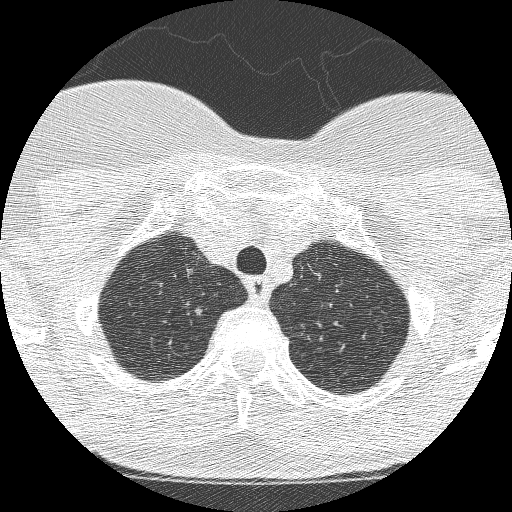
Low-dose screening chest CT, axial slice, second annual screen, lung window (W 1500 / L -600 HU), 1.25 mm slice thickness, lung (sharp) reconstruction kernel (BONE), 120 kVp, slice 210 of 250 in the series. Female, age 61 years at enrolment. Current smoker at enrolment.
- Expert-annotated lung lesion, bounding box (x1, y1, x2, y2) in pixels: (173, 295, 215, 330).
- Reader record for this screening exam (exam-level; its link to the box is not recorded): non-calcified nodule or mass ≥4 mm, right upper lobe, 11 × 8 mm, poorly defined margins, mixed attenuation, pre-existing on the prior screen: yes; interval growth: yes.
- Participant outcome: lung cancer diagnosed 28 days after this screen — adenocarcinoma, NOS, right upper lobe, poorly differentiated (G3), 12 mm at pathology.